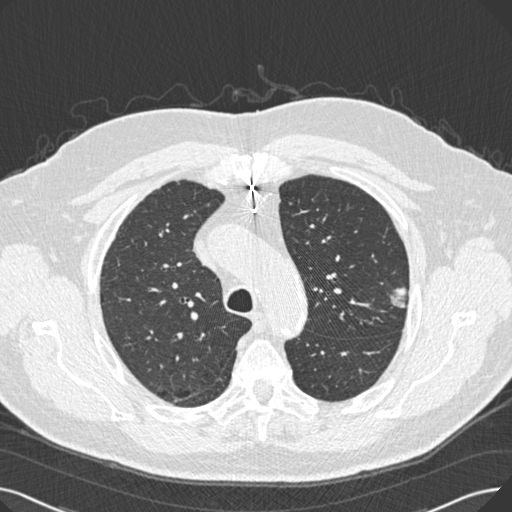
Low-dose screening chest CT, one axial slice. Slice 196 of 269 in the series (ordered by position). 120 kVp. Lung window (W 1500 / L -600 HU). 512 × 512 image matrix, field of view 370 × 370 mm.
Outlined on this slice (manually delineated by an expert):
- lesion 1 (tumor, upper lobe of left lung): bounding box [x1, y1, x2, y2] px = [390, 287, 407, 308]